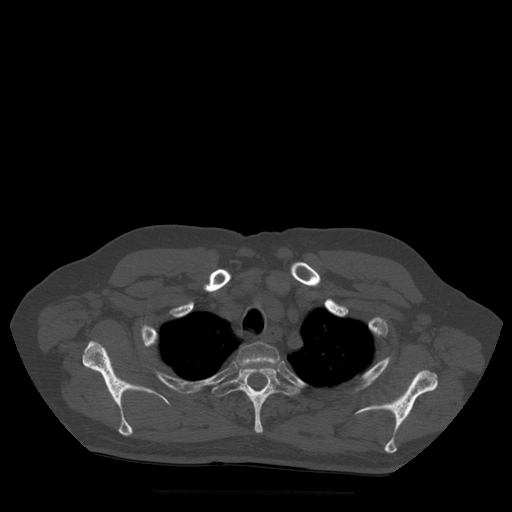
CT including the spine, one axial slice. Slice 413 of 522 in the series (ordered by position). Bone window (W 1800 / L 400 HU). 1.25 mm slice thickness. 512 × 512 image matrix, field of view 420 × 420 mm. Patient age 72 years. Case-level facts recorded for this patient, not image findings: primary cancer: prostate.
Structures marked on this image (semi-automatic segmentation, software-assisted and operator-edited):
- T2 vertebra: bounding box <237,343,280,367> (left, top, right, bottom; pixels)
- T3 vertebra: <213,364,299,434>